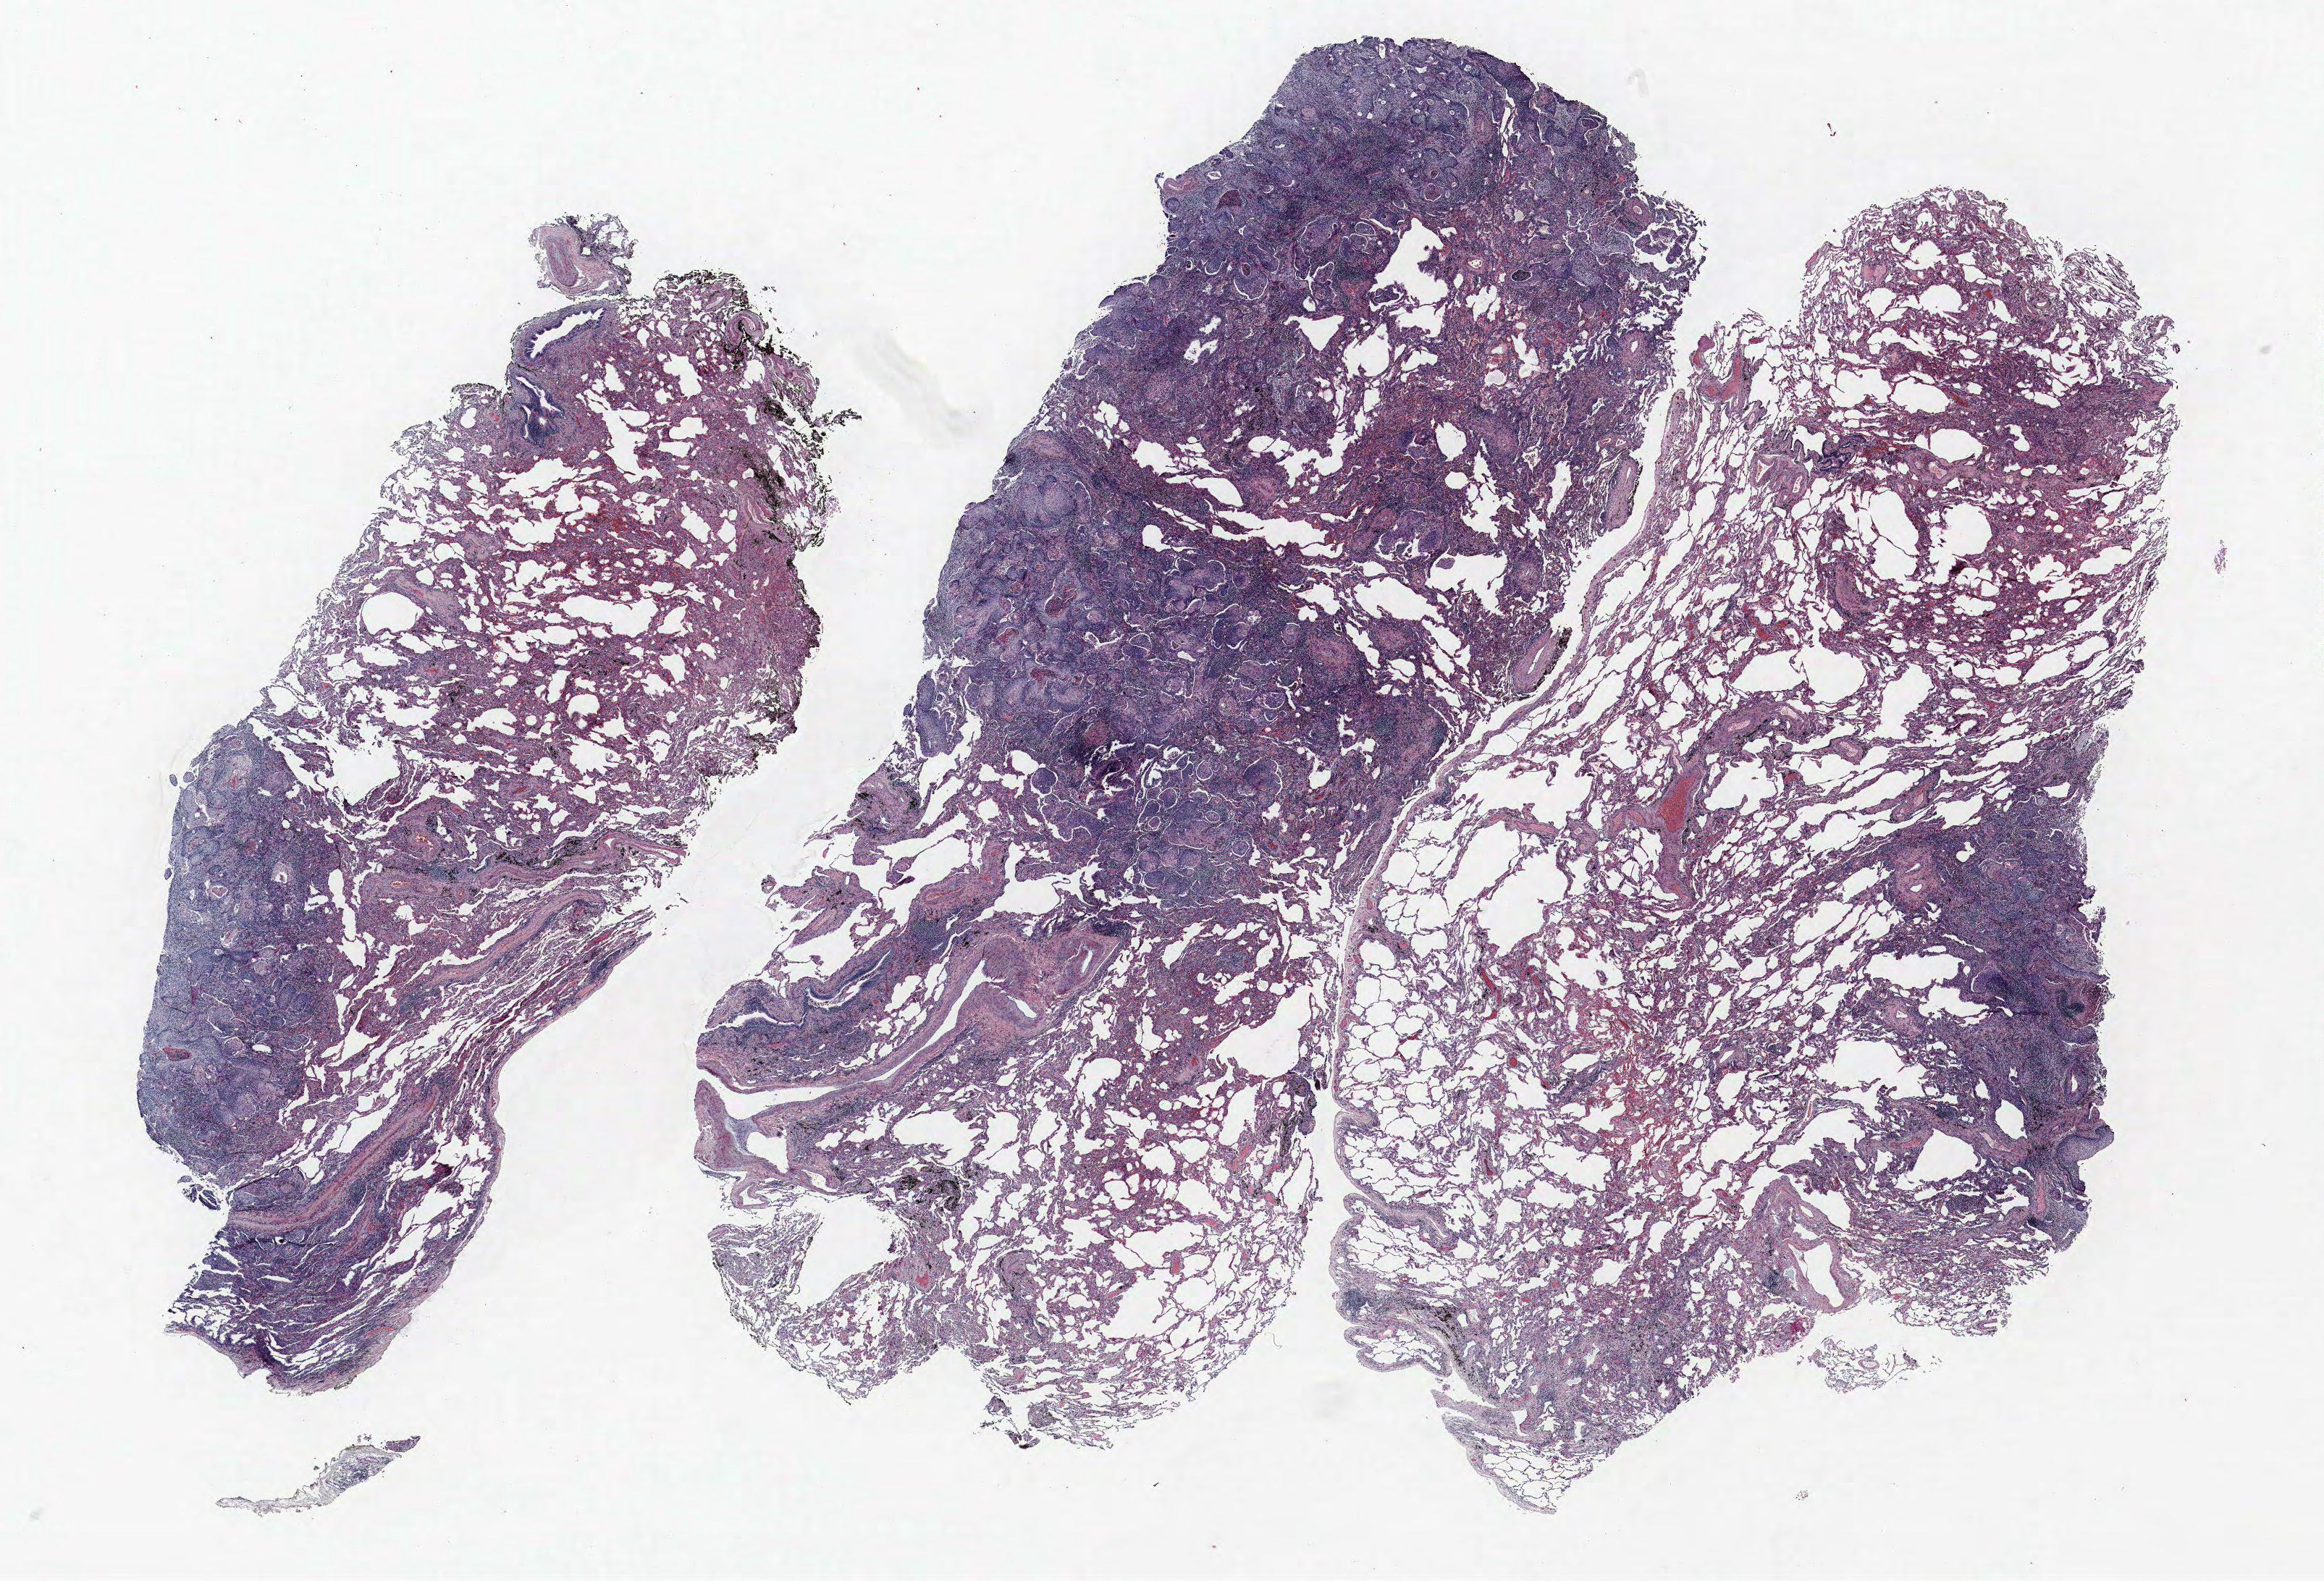
Whole-slide histology image, Hematoxylin and eosin (H&E) stained — a low-resolution overview of the entire scanned area, about 25.7 x 17.5 mm (acquisition: 40x scan); formalin-fixed paraffin-embedded (FFPE) section; lung tissue. Male, age 72 at enrolment. Former smoker at enrolment. Grade: moderately differentiated (G2).
• primary tumour location (clinical record): right lower lobe
• tumour size (pathology): 20 mm
• stage (AJCC 6th edition): IA
• participant's lung-cancer diagnosis: Squamous cell carcinoma, NOS (ICD-O-3 8070/3)